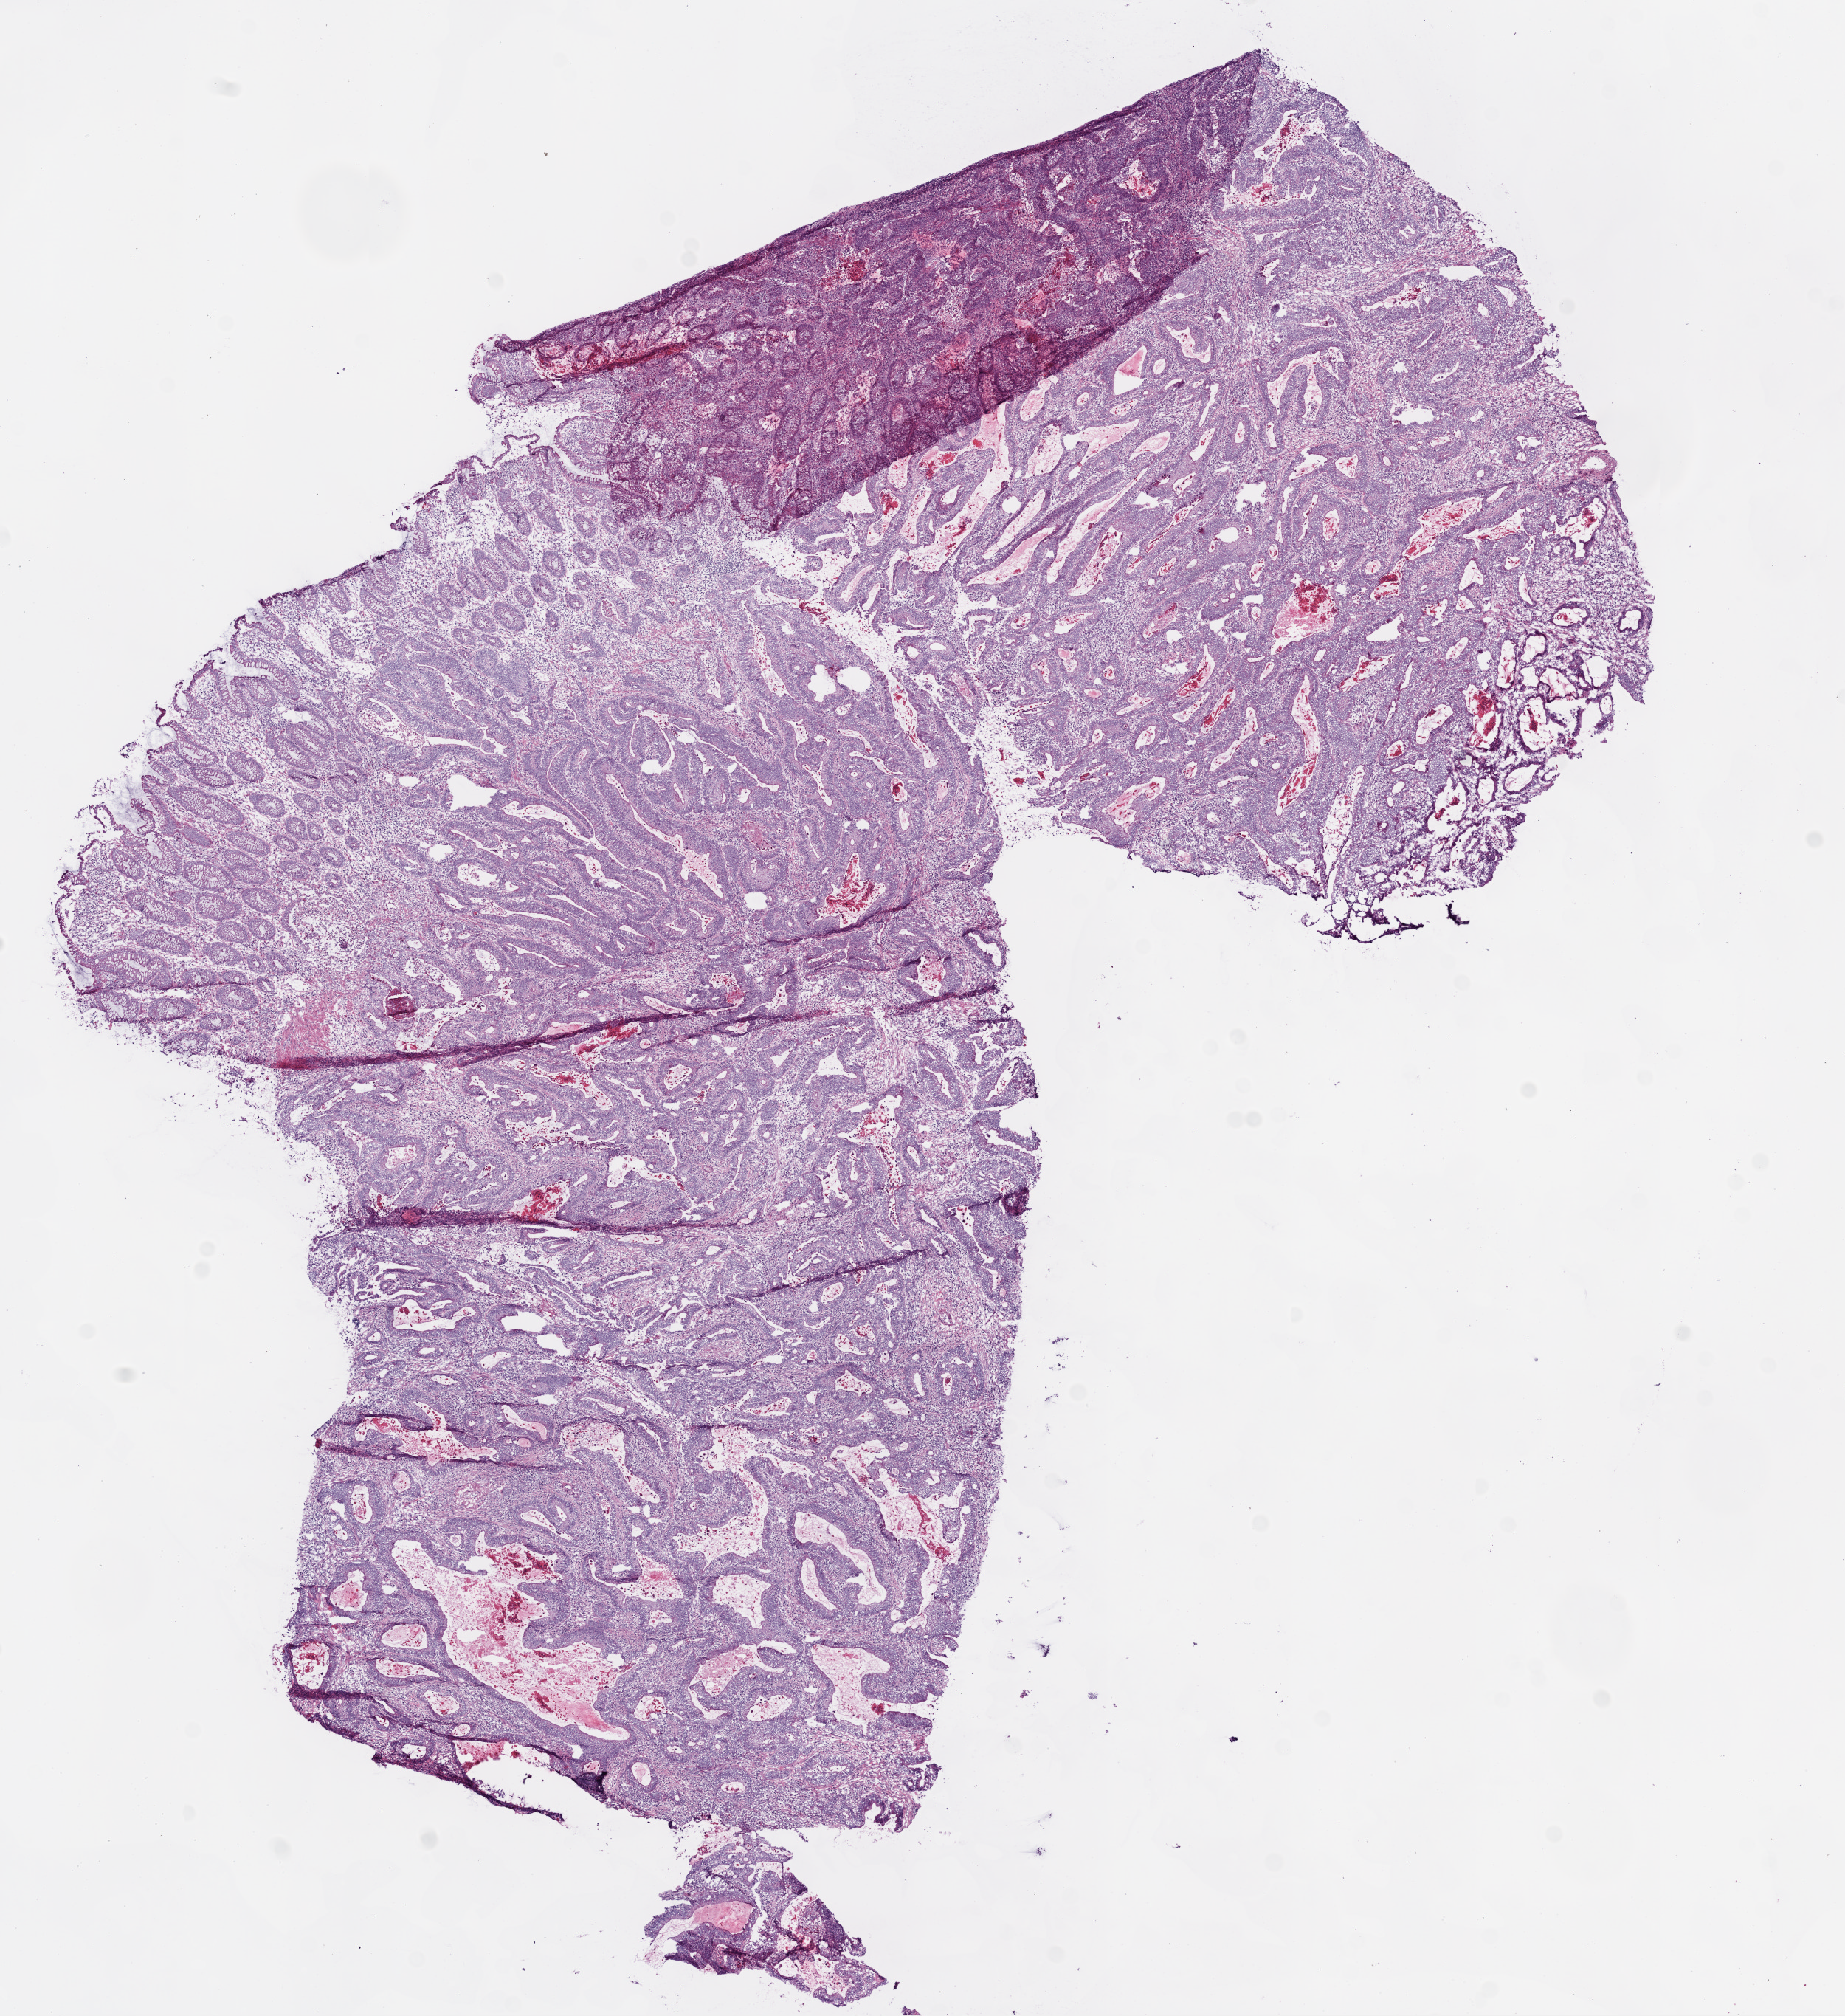
Whole-slide histology image, H&E, whole scanned area (about 10.0 x 11.0 mm, slide scanned at 20x) shown as a low-resolution overview; frozen section; primary tumour sample from the colon. Female, age 73 years at initial diagnosis. Pathologist review of this section (percent, as recorded): tumour cells 70%, tumour nuclei 70%, normal cells 15%, stromal cells 10%, necrosis 5%.
• AJCC pathologic stage: IIB (6th edition)
• pathologic diagnosis: Adenocarcinoma, NOS (ascending colon)
• lymph nodes positive (case pathology): 0 of 16 examined